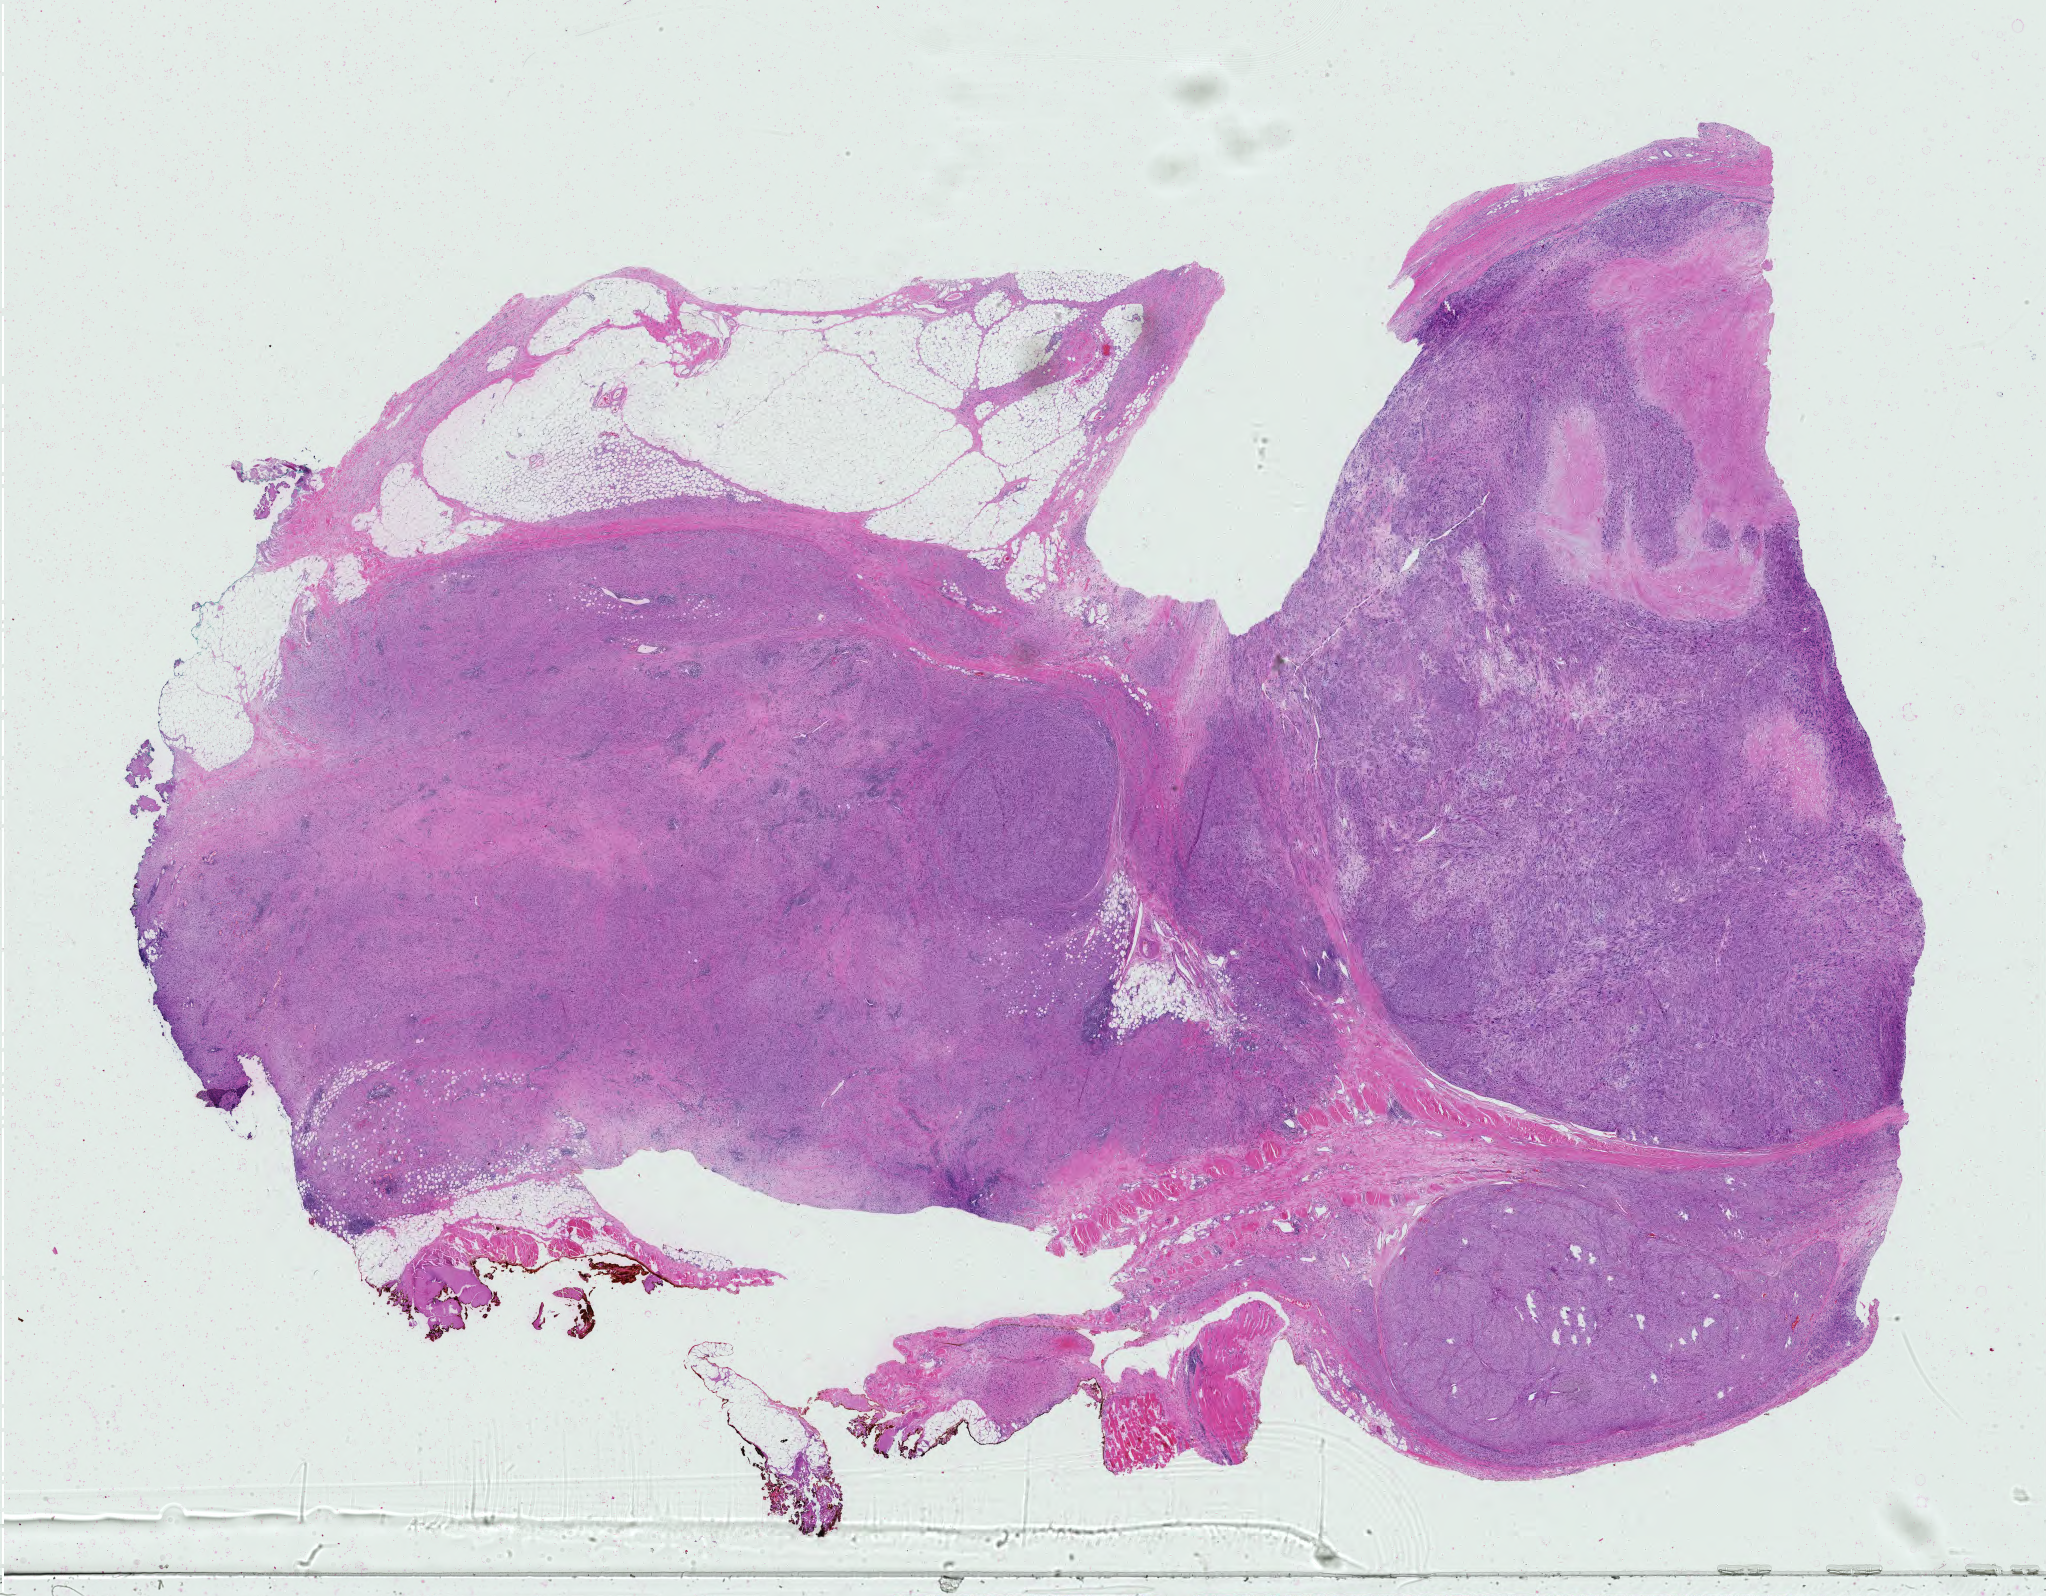
Digitized H&E tissue section (whole slide), shown as a low-resolution overview of the whole scanned area (about 29.7 x 23.1 mm, acquisition: 40x scan), formalin-fixed paraffin-embedded (FFPE) diagnostic section, primary tumour sample from the connective, subcutaneous and other soft tissues. Male, age 68 years at initial diagnosis.
Pathologic diagnosis: Undifferentiated sarcoma (connective, subcutaneous and other soft tissues of trunk, NOS).